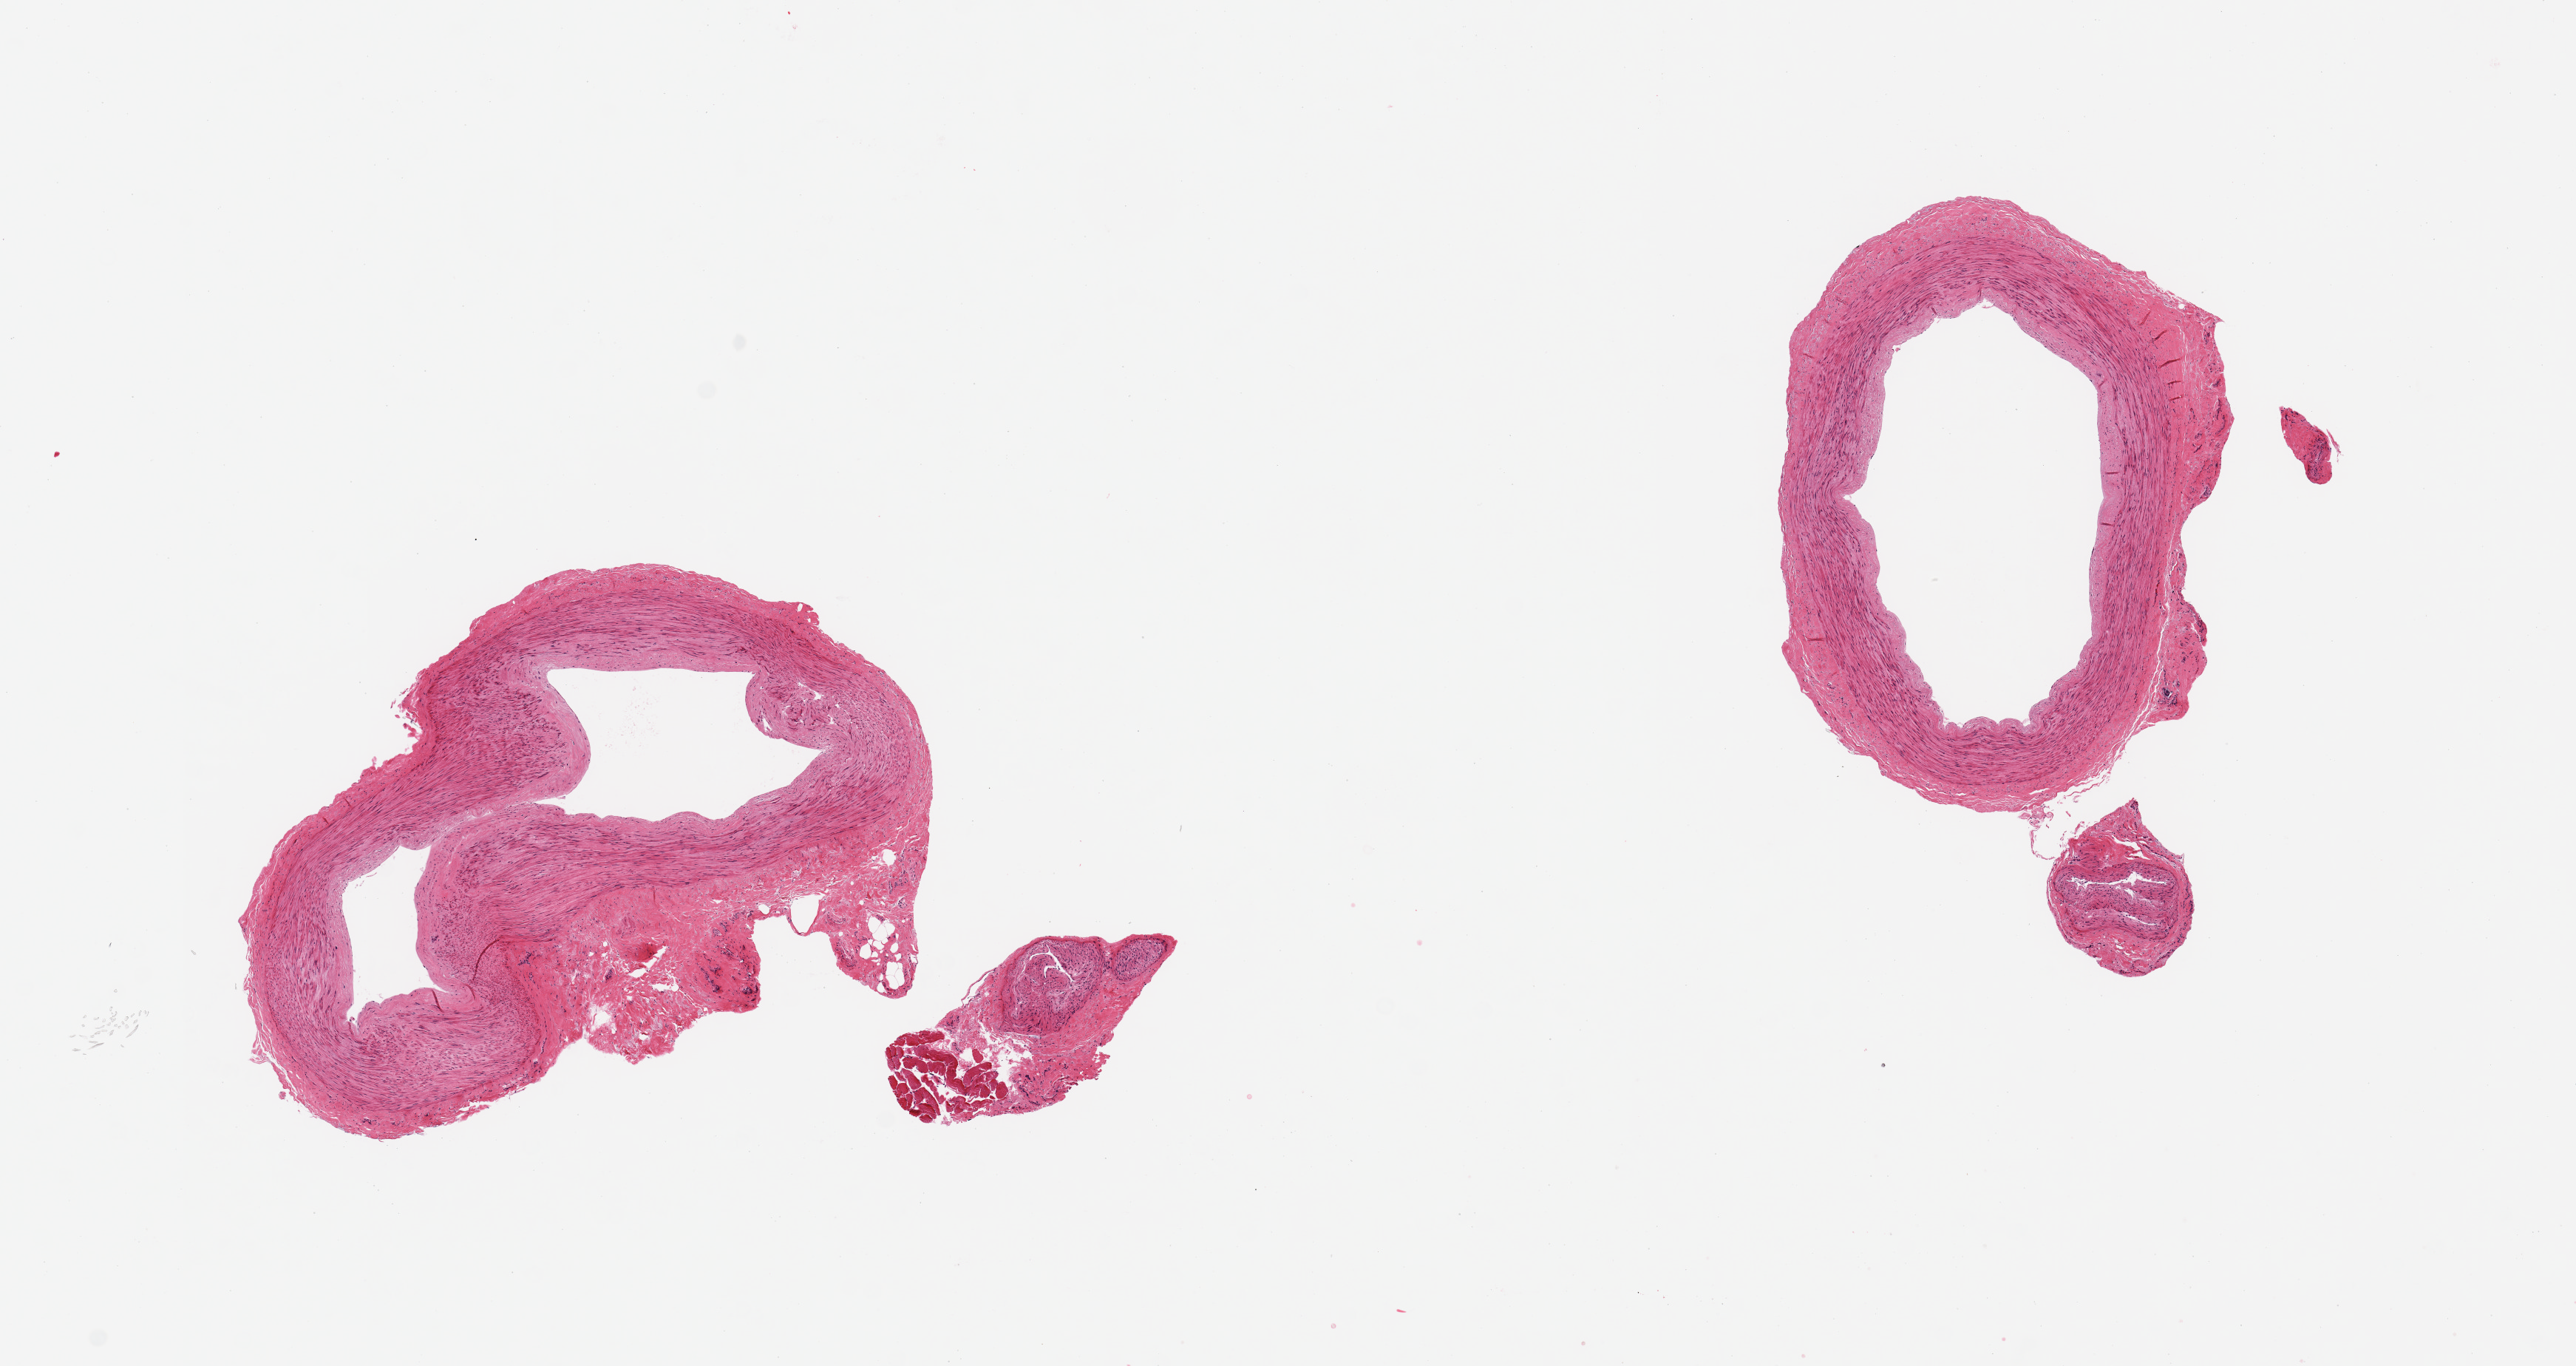
Whole-slide image, haematoxylin and eosin stain — a low-resolution overview of the entire scanned area, about 13.8 x 7.3 mm, PAXgene-fixed, paraffin-embedded tissue, sampled site (target tissue): tibial artery, tissue donor sample. Male donor.
• review note (as recorded): 2 pieces, no significant atherosis or adherent fat